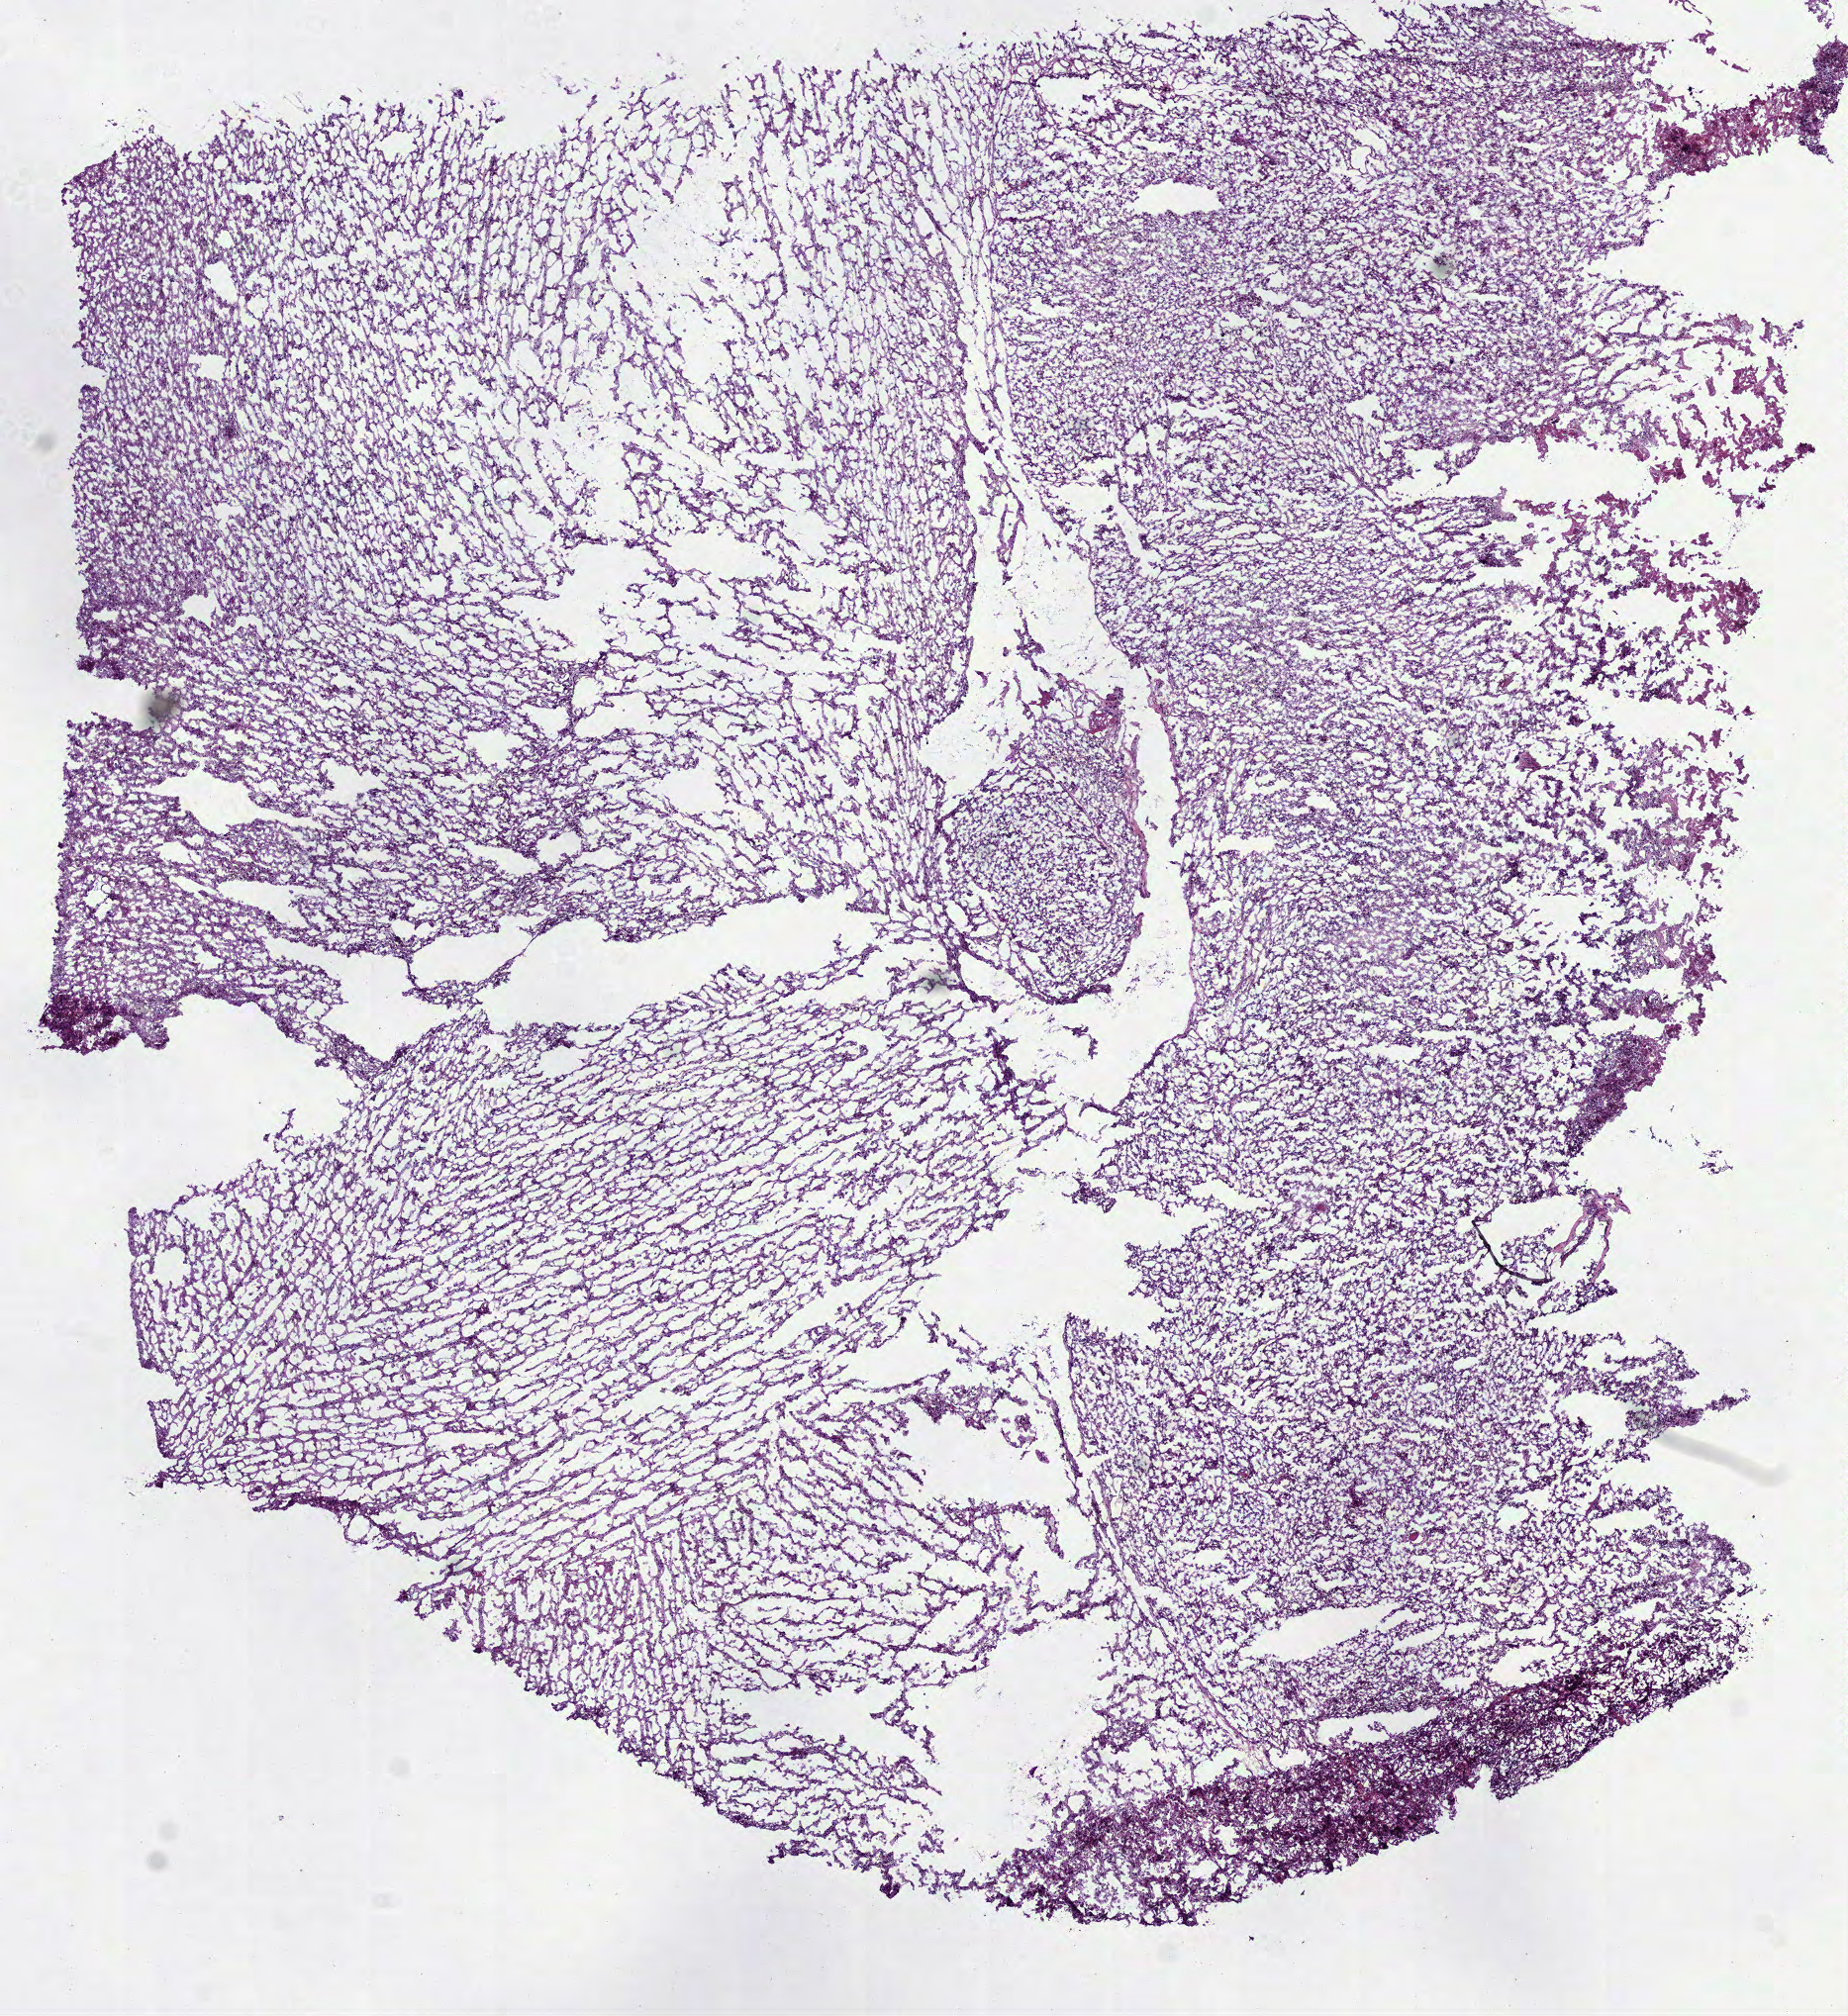
Hematoxylin and eosin (H&E) stained whole-slide image — low-resolution overview of the scanned area, about 7.5 x 8.2 mm, frozen section from the bottom of the tissue portion, sample: primary tumour, brain. Patient: male, age at initial diagnosis 54 years. Pathologist review of this section (percent, as recorded): tumour cells 95%, tumour nuclei 80%, normal cells 0%, stromal cells 0%, necrosis 5%.
• pathologic diagnosis: Glioblastoma